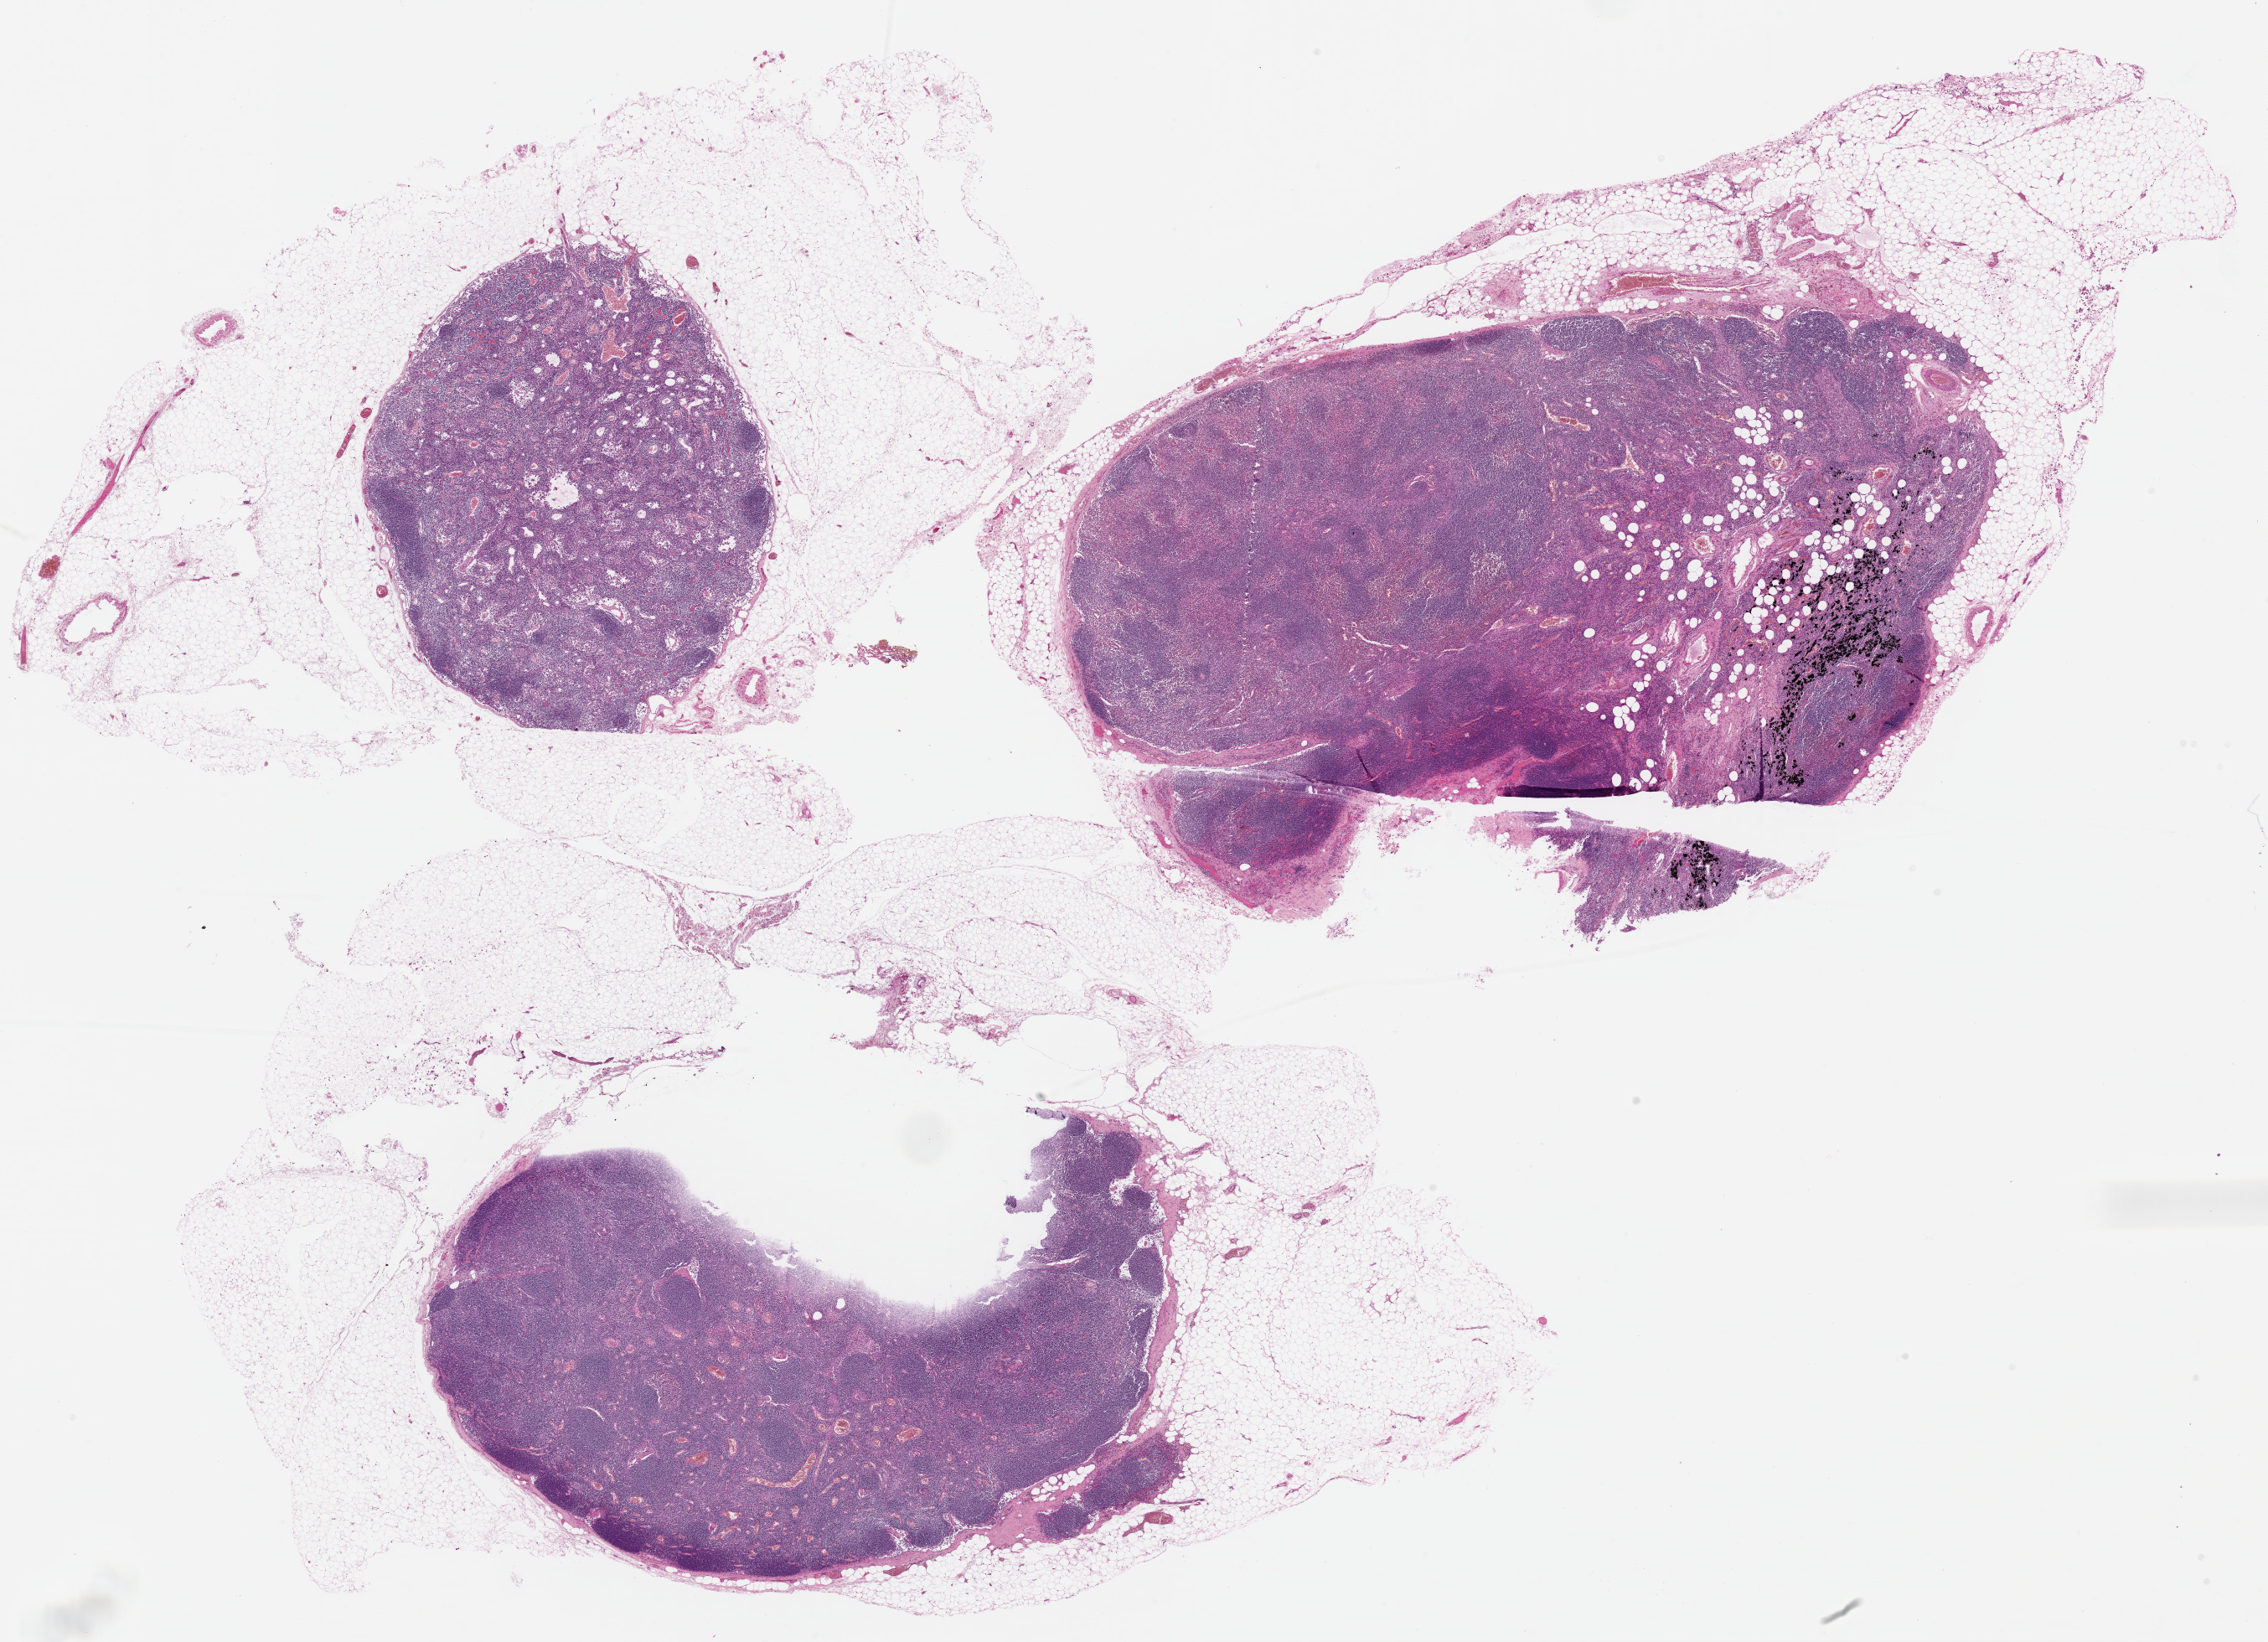
Whole-slide histology image, Hematoxylin and eosin (H&E) stained — shown as a low-resolution overview of the whole scanned area (about 21.4 x 15.5 mm). Formalin-fixed paraffin-embedded (FFPE) diagnostic section. Primary tumour sample from the skin. Patient: male, age at initial diagnosis 47 years.
* AJCC pathologic stage: III
* histologic diagnosis: Malignant melanoma, NOS